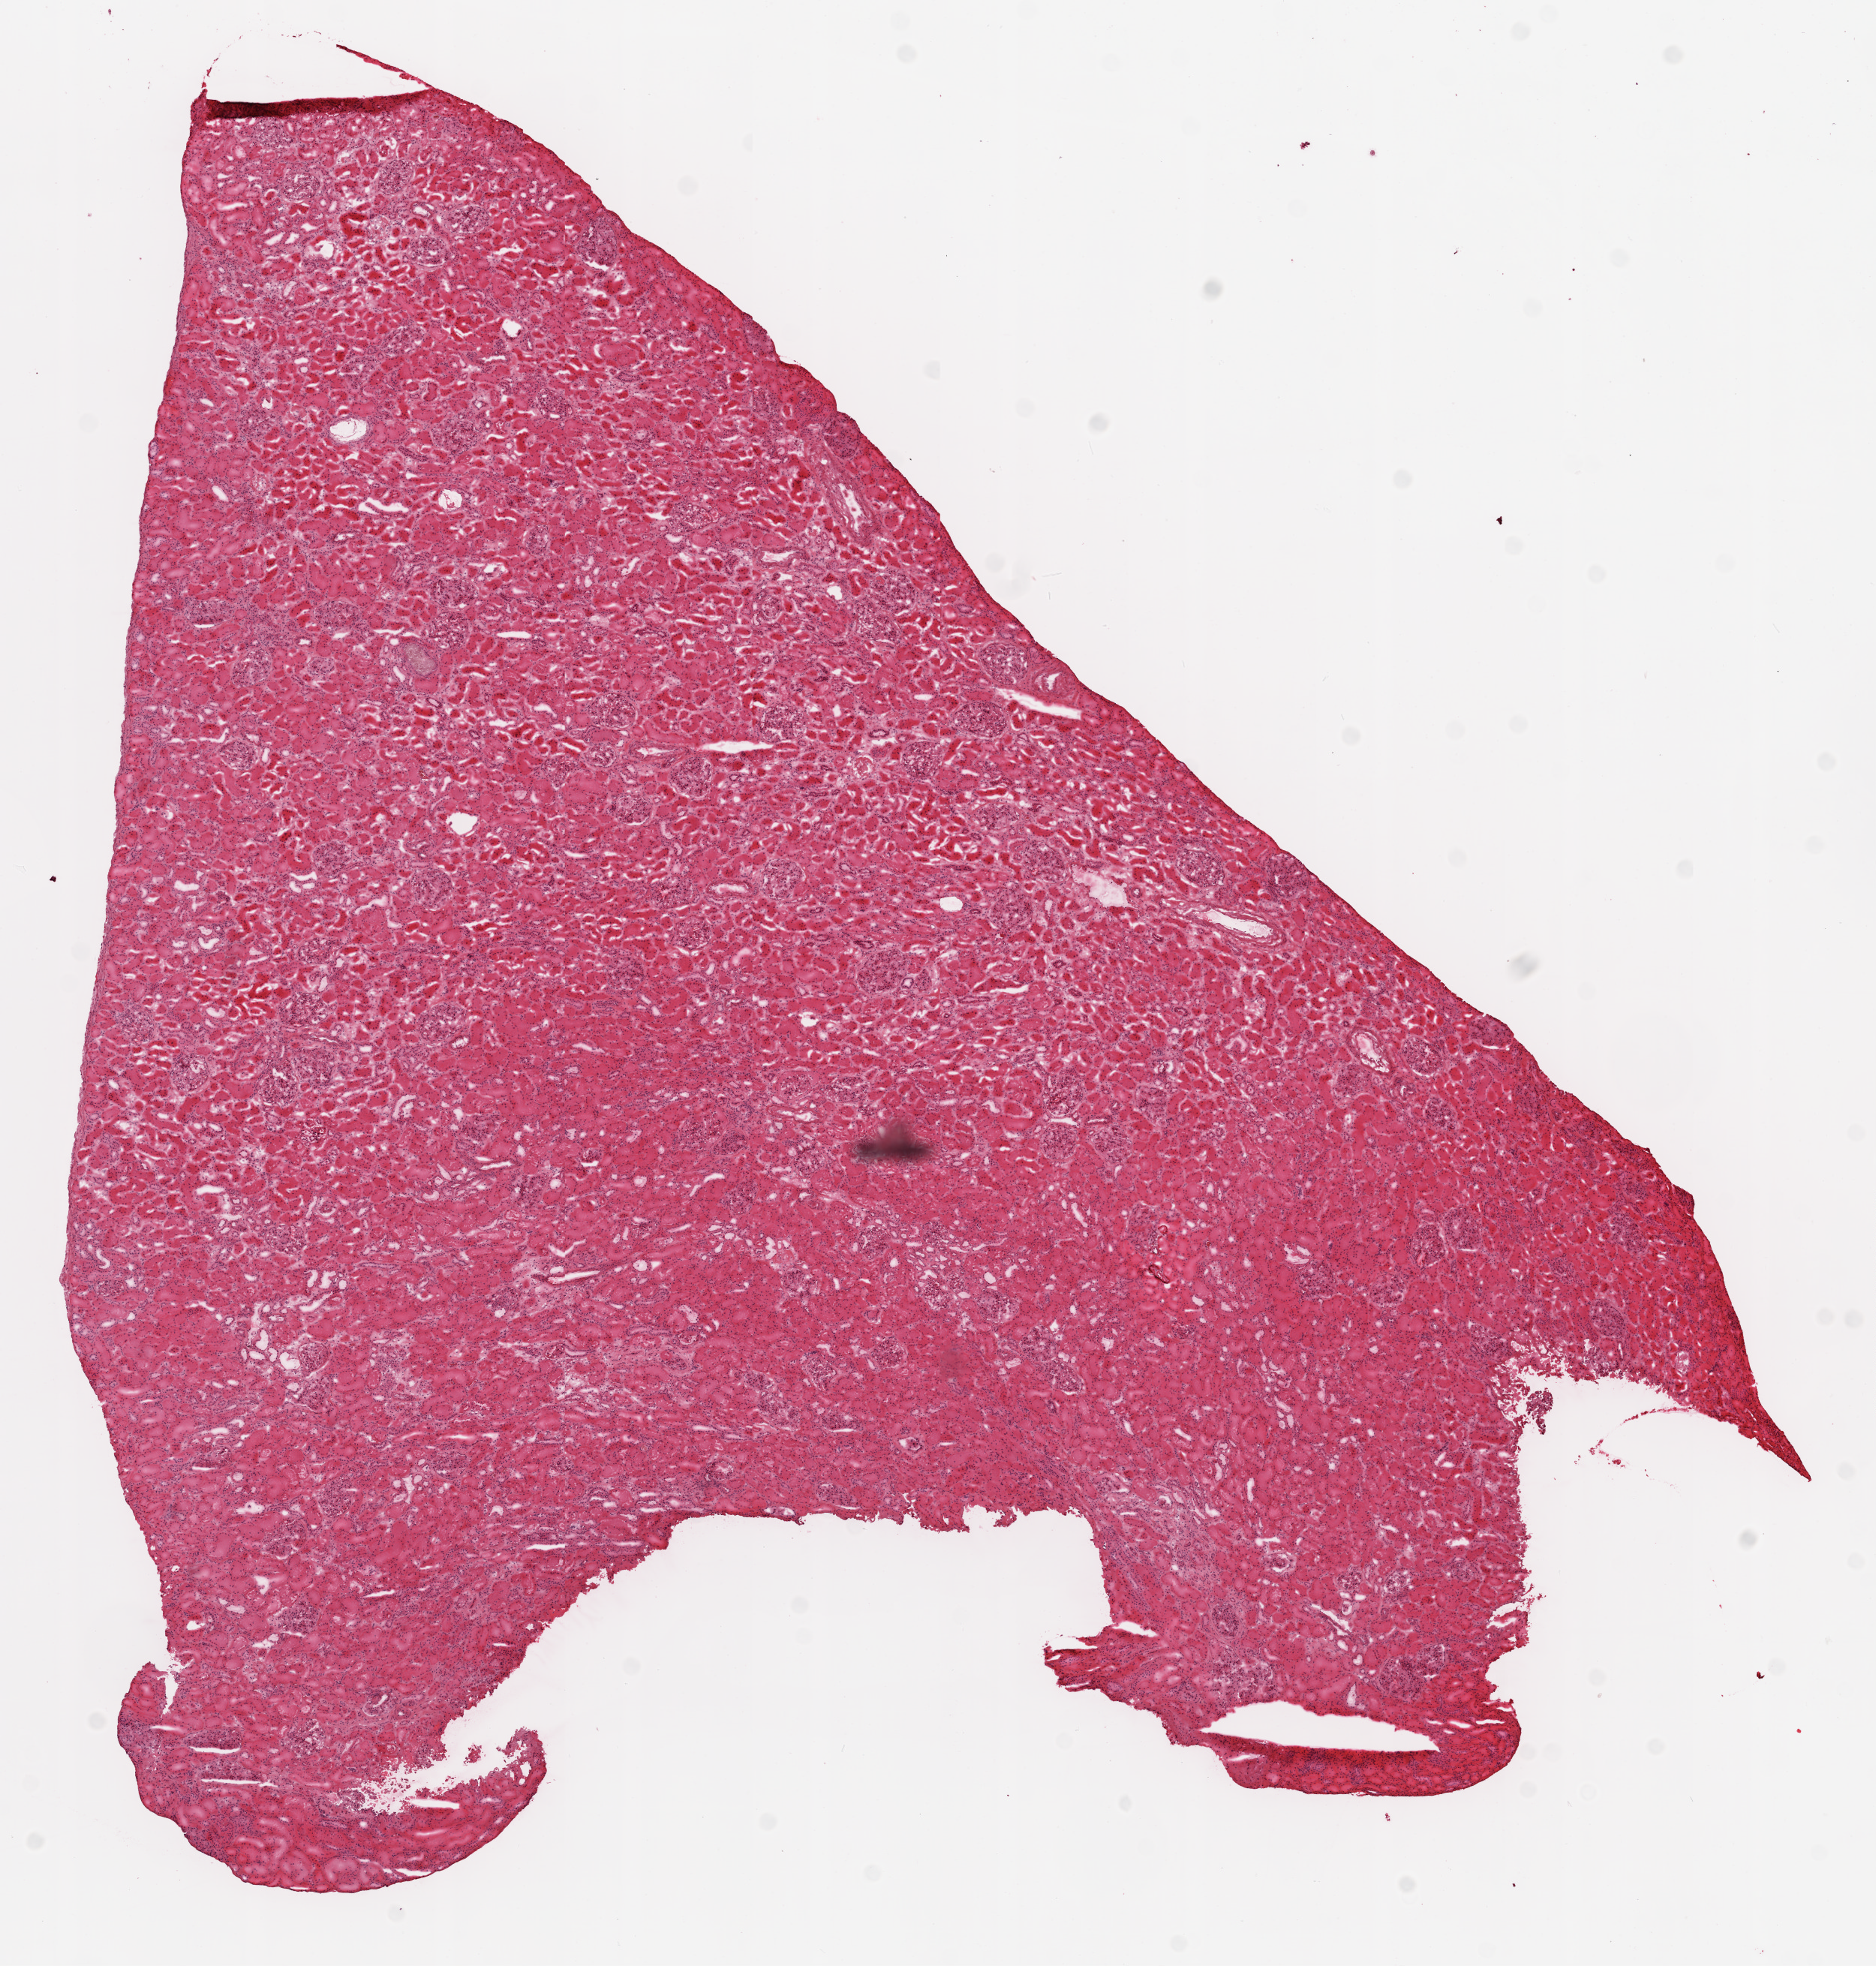
Whole-slide histology image, H&E — whole scanned area (about 10.0 x 10.5 mm, acquisition: 20x scan) shown as a low-resolution overview, frozen section from the top of the tissue portion, solid tissue normal (non-tumour tissue) sample from the kidney. Male patient; age at initial diagnosis 56 years.
* this section: solid tissue normal sample (biorepository sample class)
* patient diagnosis: Clear cell adenocarcinoma, NOS